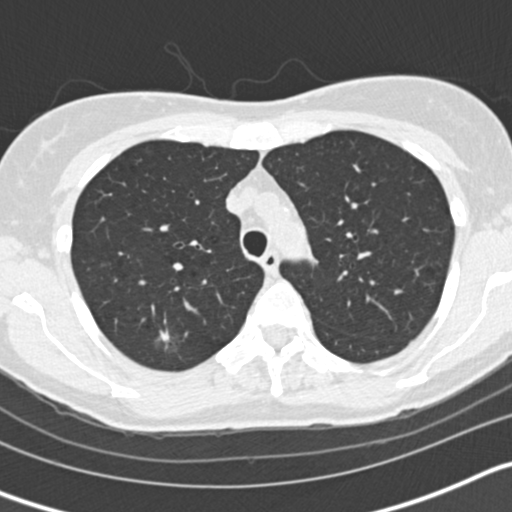
Low-dose screening chest CT, axial slice; second screening round (one year after baseline); lung window (W 1500 / L -600 HU); 2 mm slice thickness; standard (soft-tissue) reconstruction kernel (B30f); 512 × 512 image matrix. Female participant, aged 58 years at enrolment.
• Expert reader's lesion annotation, box from (x=136, y=319) to (x=193, y=366) px.
• The screening reader recorded 3 non-calcified nodules or masses ≥4 mm on this exam (right upper lobe, left upper lobe, left lower lobe); which of them this box marks is not recorded.
• Official screen result: positive, other.
• Participant outcome: lung cancer diagnosed 59 days after this screen — bronchiolo-alveolar adenocarcinoma, NOS, right upper lobe, moderately differentiated (G2), stage IA (AJCC 6th edition), 7 mm at pathology.